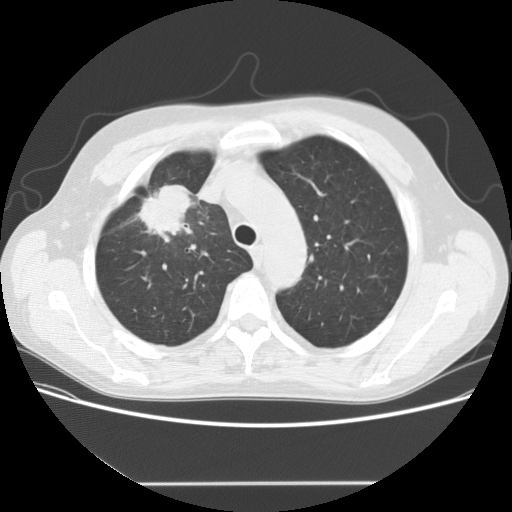
Low-dose screening chest CT, one axial slice. Slice 119 of 153 in the series (ordered by position). Lung window (W 1500 / L -600 HU). 512 × 512 image matrix.
Structures marked on this image (manually delineated by an expert):
- lesion 1 (tumor, upper lobe of right lung): box from (x=136, y=185) to (x=194, y=243) px